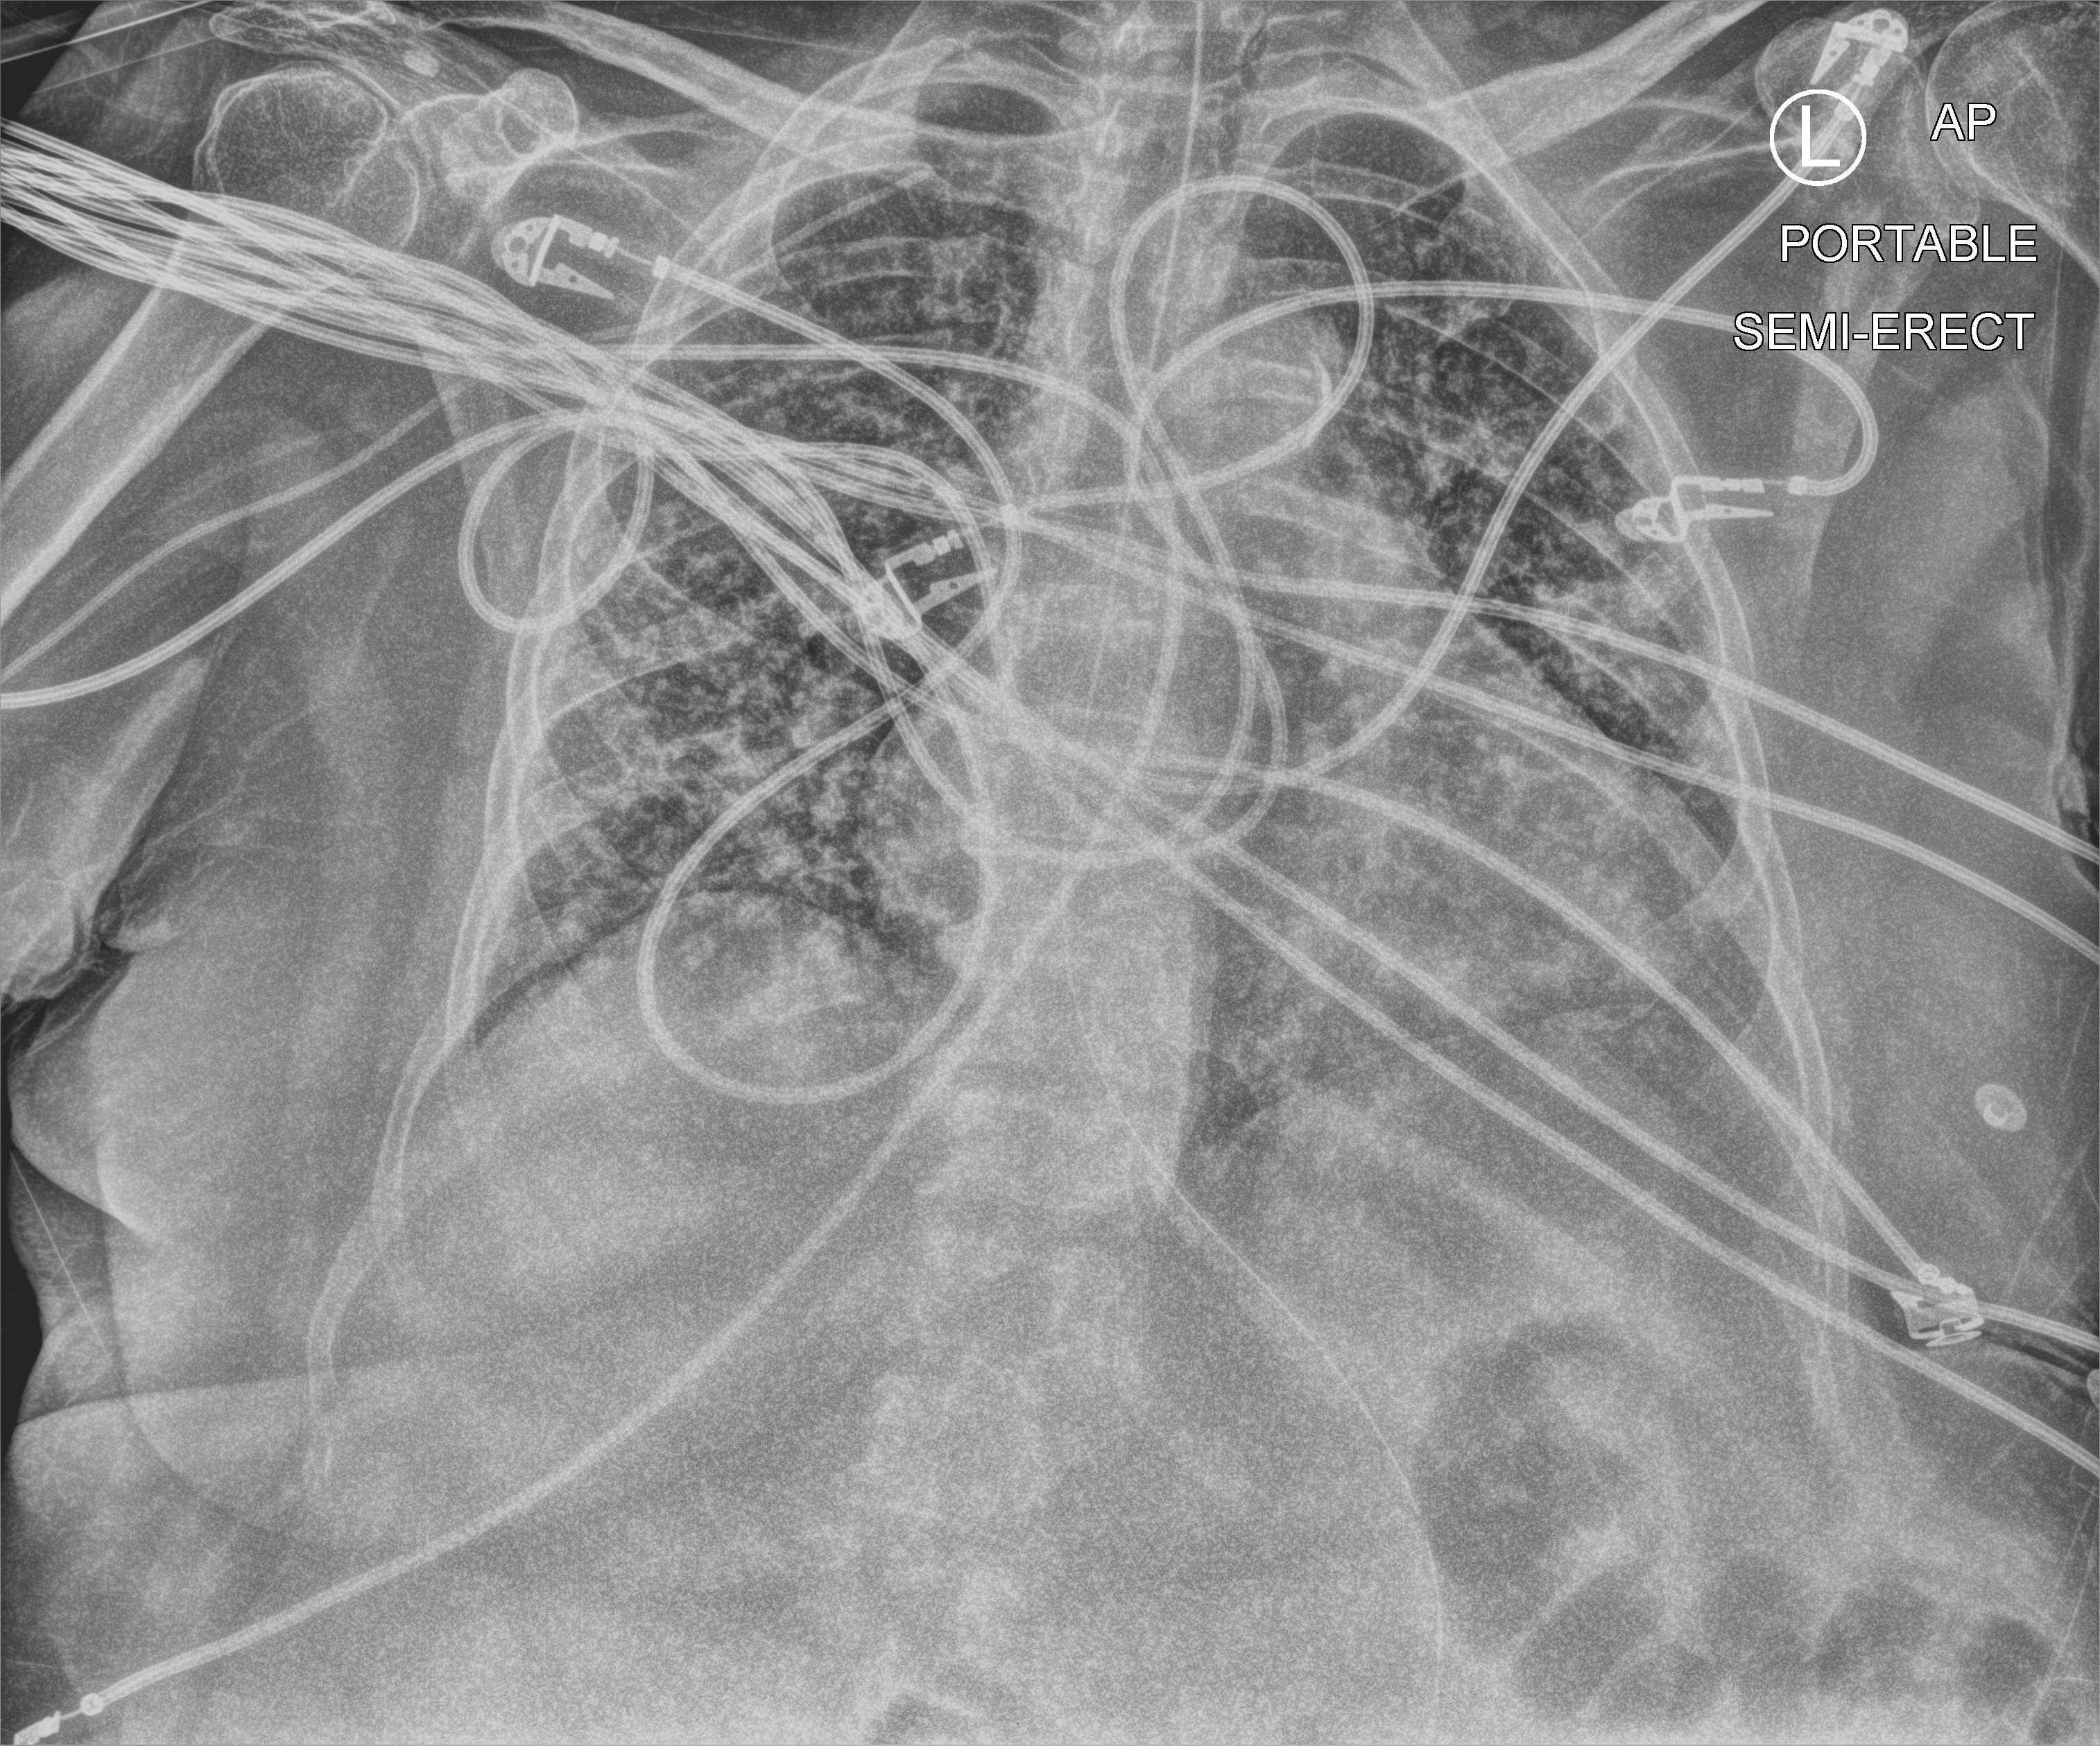
Chest X-ray (portable). Female patient hospitalised with COVID-19, age 75–90 years.
Hospital-stay facts (about this admission, not read from this image; timing relative to this image not recorded):
- admitted to intensive care during this hospital stay: yes
- mechanically ventilated during this hospital stay: yes